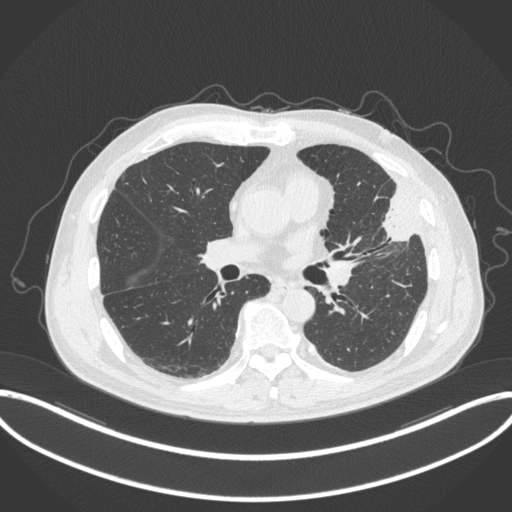
Chest CT, one axial slice. Slice 176 of 382 in the series (ordered by position). 120 kVp. Lung window (W 1500 / L -600 HU). 1 mm slice thickness. 512 × 512 image matrix, field of view 415 × 415 mm. Male patient, age 64 years. From the clinical record (not read from this slice): clinical TNM (as recorded): T4 N1 M0; histopathological grade: G3.
Structures marked on this image (bounding box drawn by a radiologist):
- lung tumour (recorded histology: adenocarcinoma): bounding box [x1, y1, x2, y2] px = [381, 180, 421, 243]